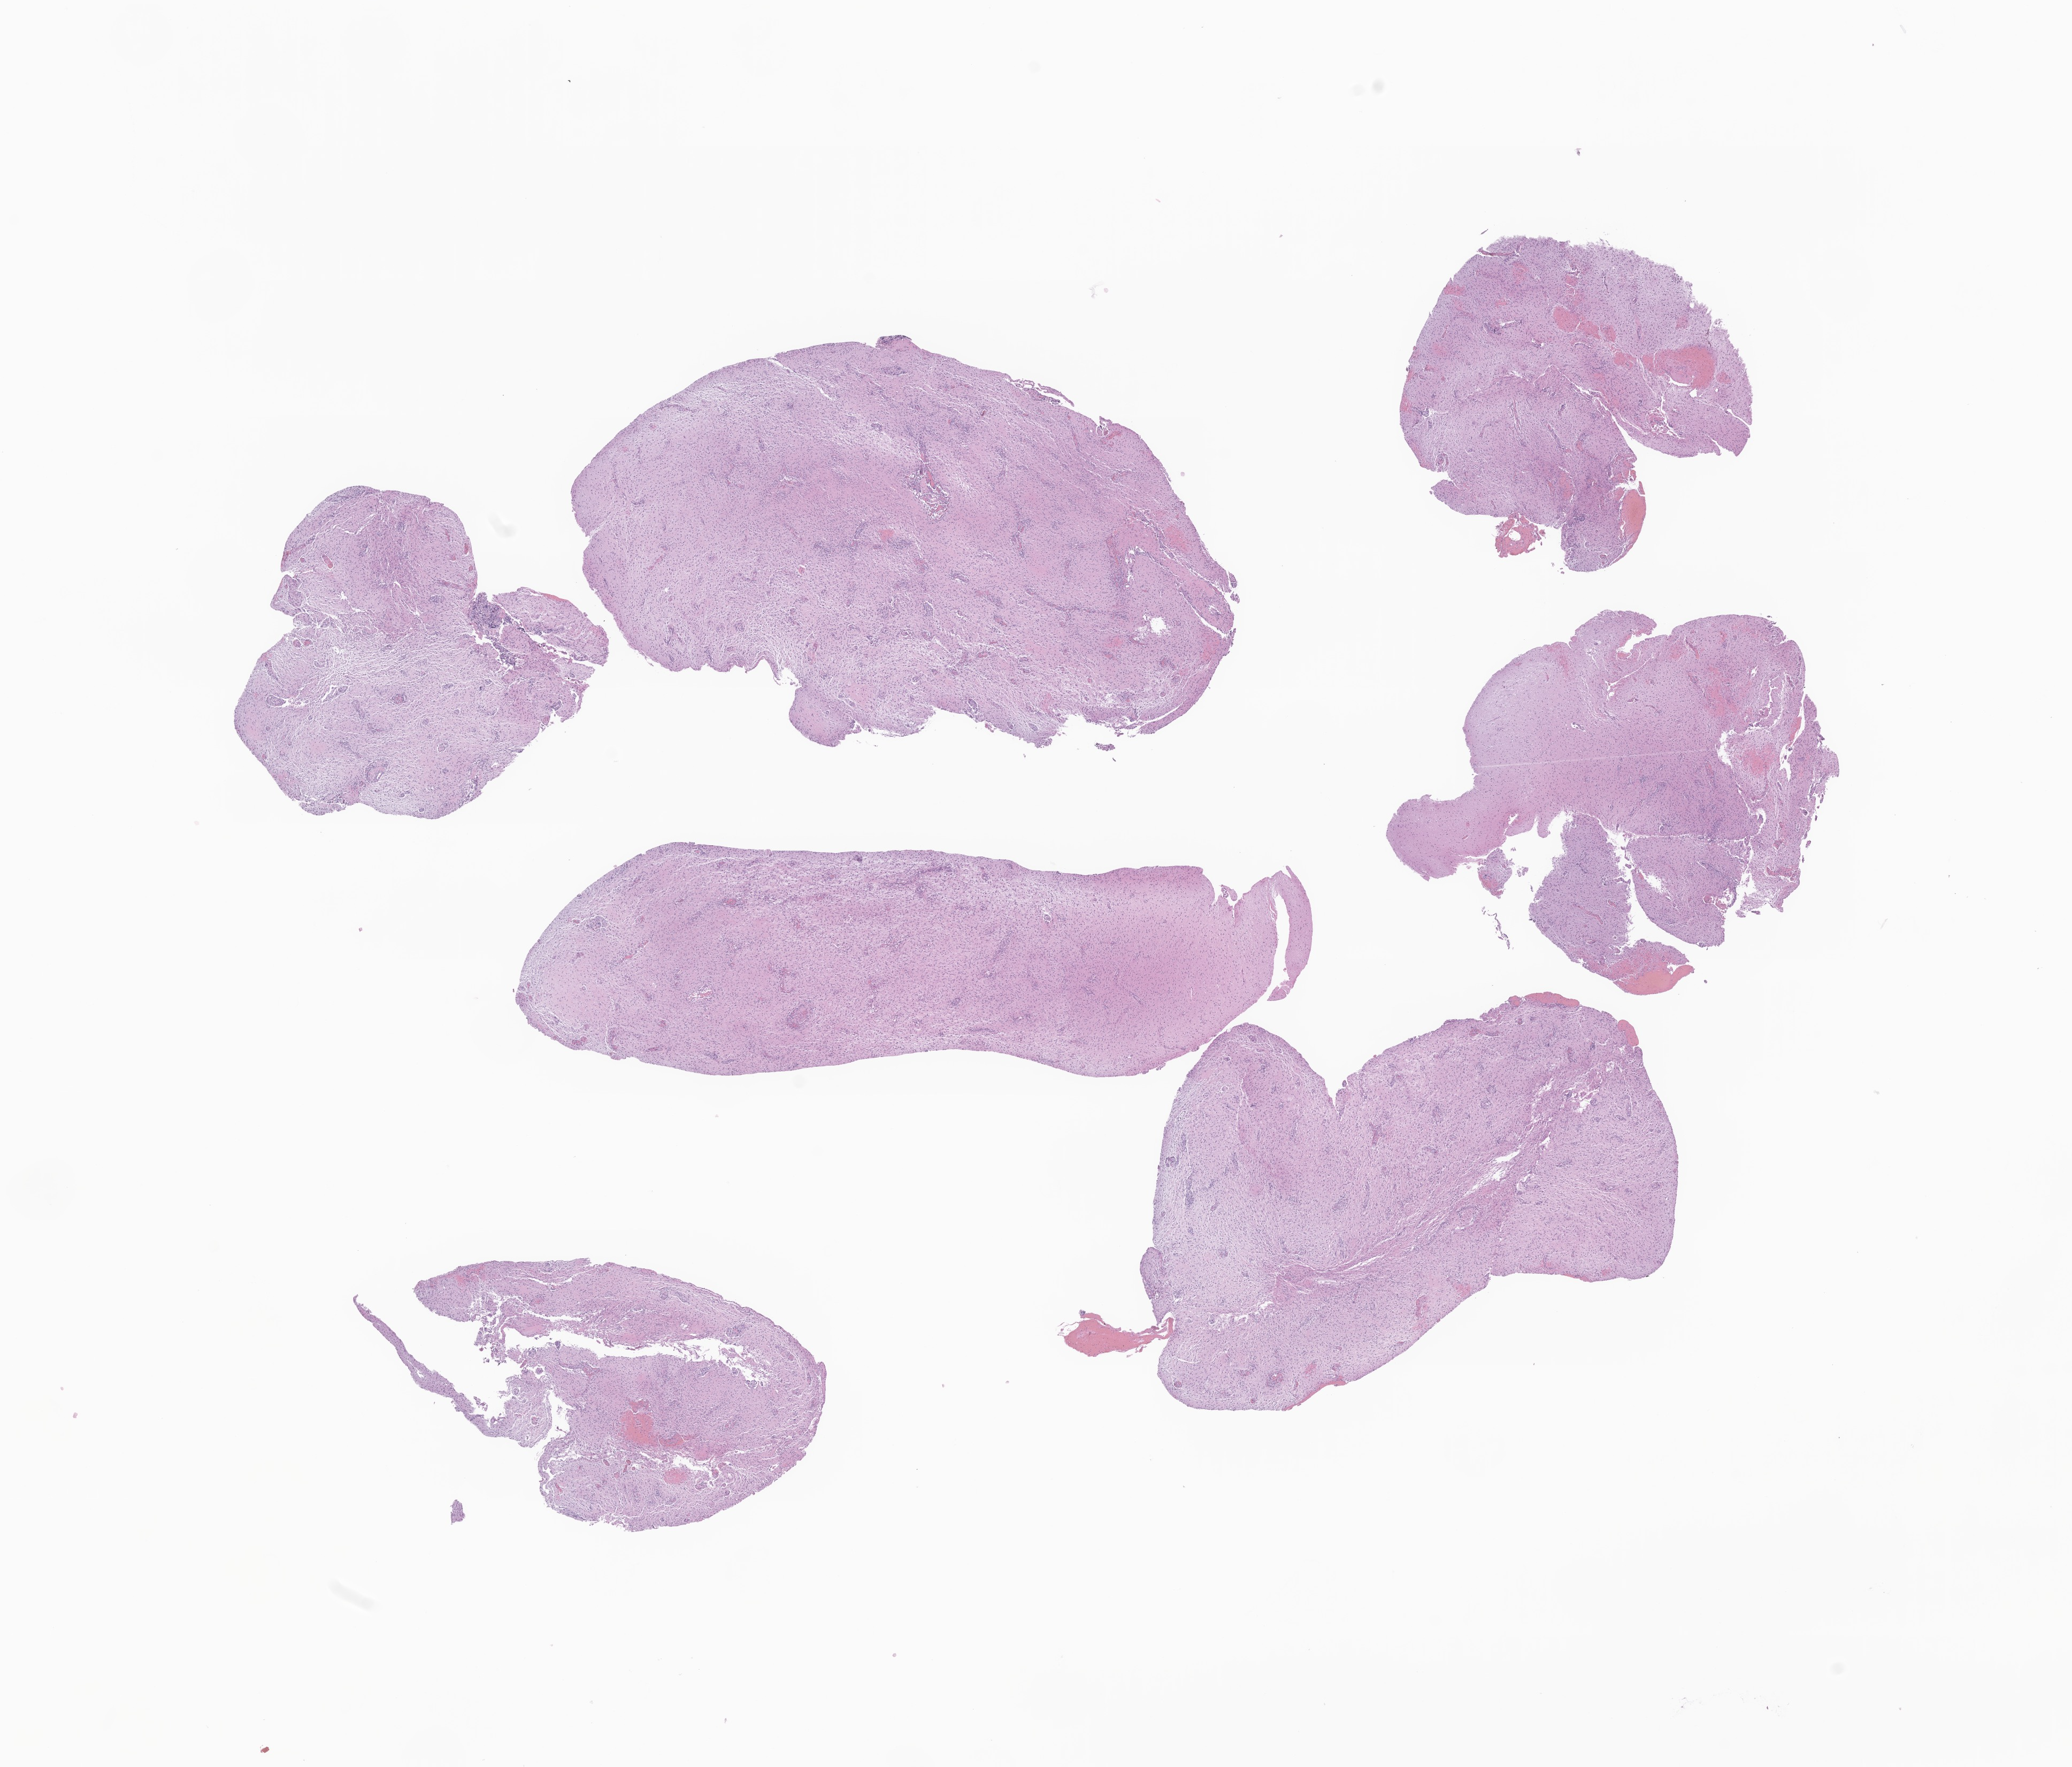
H&E whole-slide image of tumor tissue from the cerebellum — low-resolution overview of the scanned area, about 16.3 x 13.9 mm, formalin-fixed paraffin-embedded section. Patient: female, age 117 months.
- diagnosis: Pilocytic astrocytoma